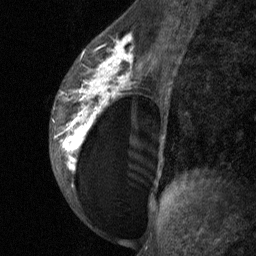
Breast MRI (dynamic contrast-enhanced), one sagittal slice; position 39 of 64 along the scan axis; dynamic contrast-enhanced study with each time point stored as its own series, time point 2 of 3 at this slice position (early post-contrast, ordered by acquisition time); 1.5 T; TE 4.8 ms, TR 27 ms; 256 × 256 image matrix, field of view 180 × 180 mm. Female patient, age 34 years. Case-level facts recorded for this patient, not image findings: setting: breast cancer imaged before/during neoadjuvant chemotherapy; receptor status: HR-positive, HER2-negative.
Outlined on this slice (semi-automatic segmentation, software-assisted and operator-edited):
- analysis volume of interest (the breast-tissue region the enhancement analysis was run in; not a lesion): bounding box [x1, y1, x2, y2] px = [49, 23, 157, 197]
- tumour enhancement mask (voxels above the 90 % enhancement threshold inside the analysis volume of interest): [54, 34, 132, 172]